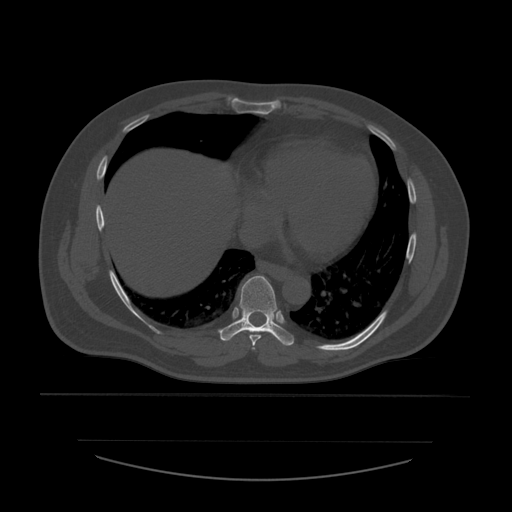
CT including the spine, one axial slice; slice 342 of 532 in the series (ordered by position); reconstruction kernel STANDARD; bone window (W 1800 / L 400 HU); 1.25 mm slice thickness; 512 × 512 image matrix, field of view 441 × 441 mm. Patient age 44 years. Case-level facts recorded for this patient, not image findings: primary cancer: soft tissue sarcoma.
Structures marked on this image (semi-automatically segmented with operator editing):
- T6 vertebra: box from (x=252, y=348) to (x=256, y=350) px
- T7 vertebra: (x=249, y=335)–(x=262, y=346)
- T8 vertebra: (x=219, y=276)–(x=295, y=346)